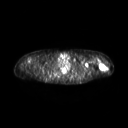
FDG PET of an extremity soft-tissue mass (from a PET/CT study), one axial slice; slice 205 of 267 in the series (ordered by position); 3.27 mm slice thickness; 128 × 128 image matrix, field of view 600 × 600 mm. Female patient, age 28 years. Case-level facts recorded for this patient, not image findings: histological type: malignant fibrous histiocytoma; grade: low; site of the primary tumour: left arm.
Outlined on this slice (expert contour drawn on MRI and transferred to this co-registered scan by the dataset authors):
- gross tumour volume (mass): bounding box (x1, y1, x2, y2) in pixels: (98, 62, 107, 70)